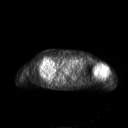
FDG PET of an extremity soft-tissue mass (from a PET/CT study), one axial slice. Position 146 of 267 along the scan axis. 3.27 mm slice thickness. 128 × 128 image matrix, field of view 700 × 700 mm. Female patient, age 83 years. Case-level facts recorded for this patient, not image findings: histological type: pleiomorphic leiomyosarcoma; grade: high; site of the primary tumour: left biceps.
Annotated regions visible in this slice (expert contour drawn on MRI and transferred to this co-registered scan by the dataset authors):
- gross tumour volume including surrounding oedema: bounding box [x1, y1, x2, y2] px = [93, 64, 108, 76]
- gross tumour volume (mass): [93, 64, 108, 76]